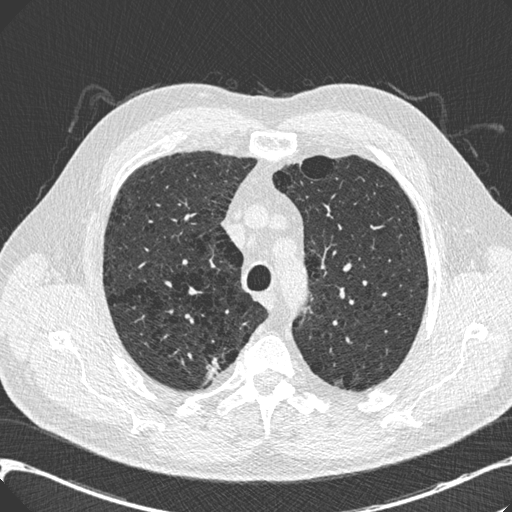
Chest CT (low-dose screening protocol), one axial image; third screening round (two years after baseline); lung window (W 1500 / L -600 HU); slice 46 of 197 in the series. Male, age 68 years at enrolment. Current smoker at enrolment.
Expert-annotated lung lesion, bounding box [x1, y1, x2, y2] px = [189, 348, 234, 391]. The screening reader recorded 3 non-calcified nodules or masses ≥4 mm on this exam; which of them this box marks is not recorded.